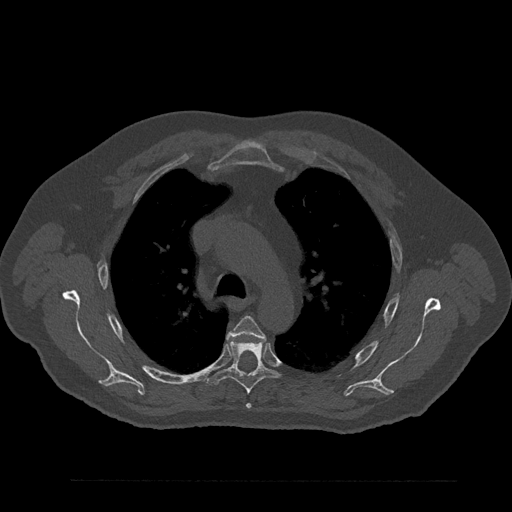
CT including the spine, one axial slice. Position 611 of 797 along the scan axis. Reconstruction kernel Br40s/3. 120 kVp. Bone window (W 1800 / L 400 HU). 0.5 mm slice thickness. 512 × 512 image matrix, field of view 430 × 430 mm. Patient: male, 61 years. From the clinical record (not read from this slice): primary cancer: prostate.
Annotated regions visible in this slice (semi-automatic segmentation, software-assisted and operator-edited):
- T4 vertebra: box from (x=227, y=316) to (x=266, y=409) px
- T5 vertebra: (x=207, y=340)–(x=278, y=394)